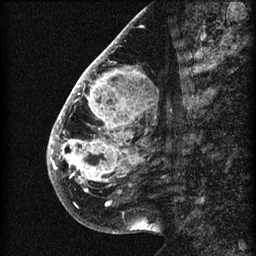
Breast MRI (dynamic contrast-enhanced), one sagittal slice; slice 23 of 60 in the series (ordered by position); 3 images stored at this slice position (order not interpretable as contrast timing); 1.5 T; TE 4.2 ms, TR 22.7 ms; 2 mm slice thickness; 256 × 256 image matrix. Patient: female, 48 years. From the clinical record (not read from this slice): setting: breast cancer imaged before/during neoadjuvant chemotherapy; receptor status: triple-negative.
Structures marked on this image (semi-automatic segmentation, software-assisted and operator-edited):
- analysis volume of interest (the breast-tissue region the enhancement analysis was run in; not a lesion): bounding box (x1, y1, x2, y2) in pixels: (47, 30, 173, 207)
- tumour enhancement mask (voxels above the 90 % enhancement threshold inside the analysis volume of interest): (48, 51, 136, 192)